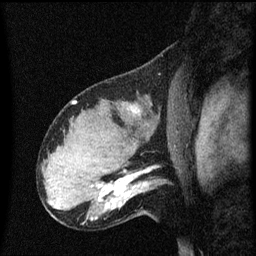
Breast MRI (dynamic contrast-enhanced), one sagittal slice; slice 42 of 60 in the series (ordered by position); dynamic contrast-enhanced series, image 2 of 3 at this slice position (ordered by acquisition); 1.5 T; TE 4.2 ms, TR 8.4 ms; 256 × 256 image matrix. Patient: female, 31 years. From the clinical record (not read from this slice): setting: breast cancer imaged before/during neoadjuvant chemotherapy; receptor status: HR-positive, HER2-negative.
Structures marked on this image (semi-automatic segmentation, software-assisted and operator-edited):
- analysis volume of interest (the breast-tissue region the enhancement analysis was run in; not a lesion): bounding box (x1, y1, x2, y2) in pixels: (102, 166, 169, 219)
- tumour enhancement mask (voxels above the 70 % enhancement threshold inside the analysis volume of interest): (107, 170, 148, 207)